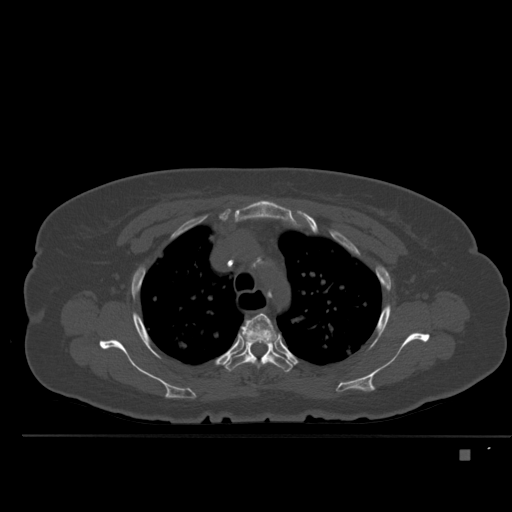
CT including the spine, one axial slice. Position 372 of 477 along the scan axis. Bone window (W 1800 / L 400 HU). 1.5 mm slice thickness. 512 × 512 image matrix, field of view 422 × 422 mm. Female patient, age 74 years. From the clinical record (not read from this slice): primary cancer: colon.
Structures marked on this image (semi-automatically segmented with operator editing):
- T3 vertebra: bounding box (x1, y1, x2, y2) in pixels: (240, 313, 279, 369)
- T4 vertebra: (225, 333, 293, 373)